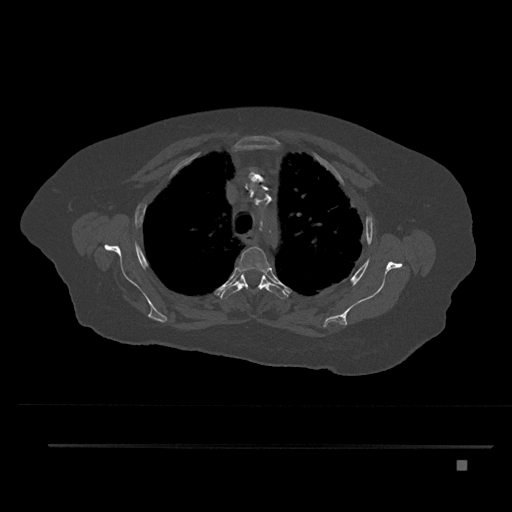
CT including the spine, one axial slice; slice 617 of 797 in the series (ordered by position); reconstruction kernel Br40s/3; 120 kVp; bone window (W 1800 / L 400 HU); 0.5 mm slice thickness; 512 × 512 image matrix, field of view 437 × 437 mm. Patient: female, 76 years. Case-level facts recorded for this patient, not image findings: primary cancer: lung.
Annotated regions visible in this slice (semi-automatic segmentation, software-assisted and operator-edited):
- T3 vertebra: bounding box <237,246,271,273> (left, top, right, bottom; pixels)
- T4 vertebra: <219,270,289,299>